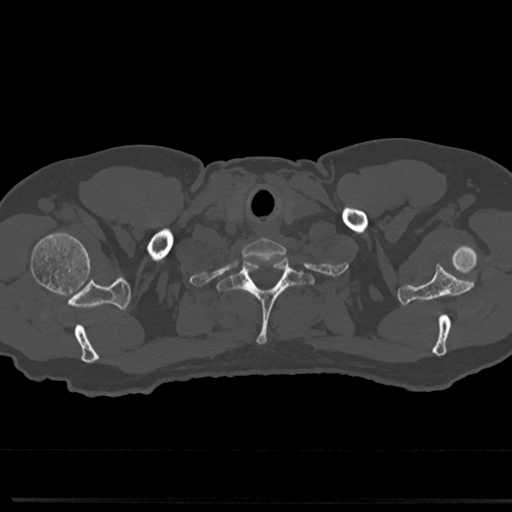
CT including the spine, one axial slice; slice 680 of 817 in the series (ordered by position); reconstruction kernel Br40s/3; bone window (W 1800 / L 400 HU); 0.5 mm slice thickness; 512 × 512 image matrix. Male patient, age 61 years. From the clinical record (not read from this slice): primary cancer: prostate.
Annotated regions visible in this slice (semi-automatically segmented with operator editing):
- T1 vertebra: bounding box [x1, y1, x2, y2] px = [222, 253, 310, 345]